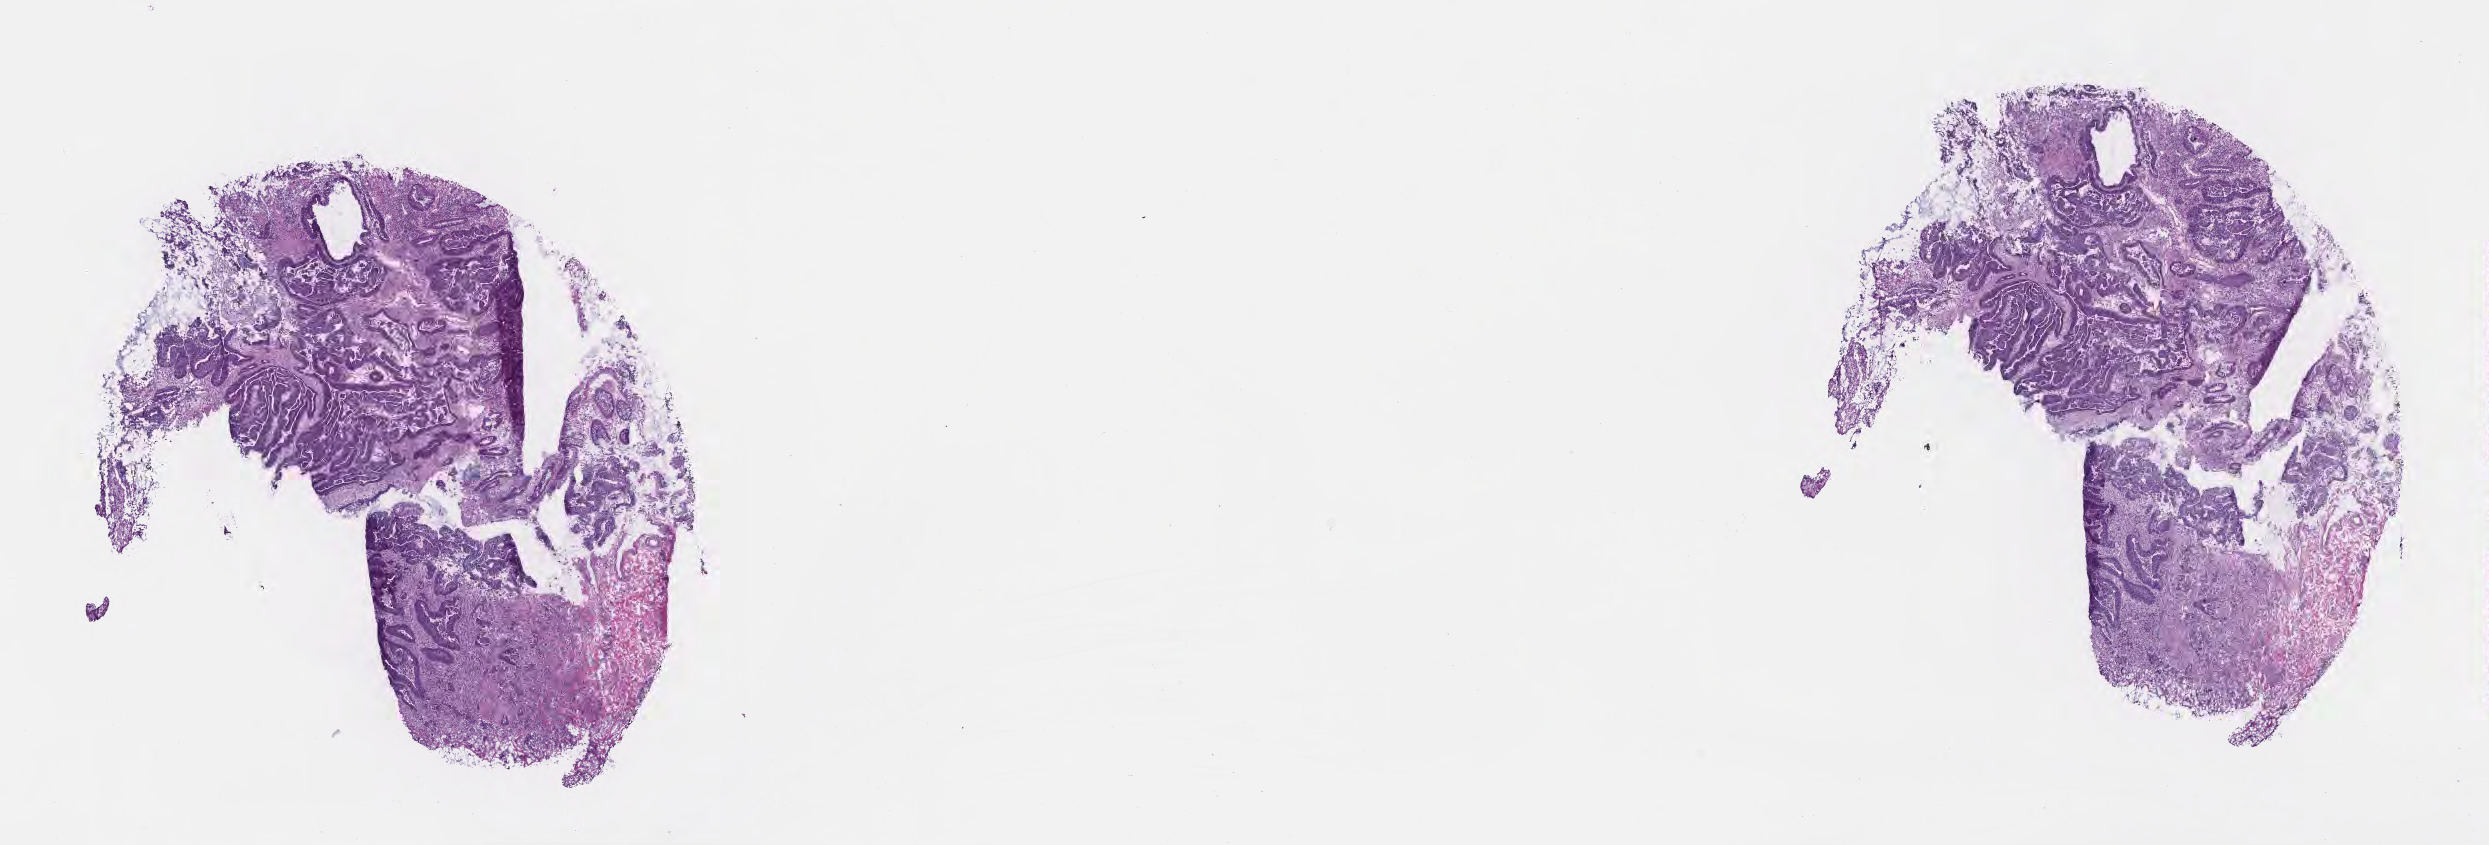
Digitized haematoxylin and eosin-stained section, low-resolution overview of the scanned area, about 20.1 x 6.8 mm. Frozen section. Specimen: primary tumor. Anatomic site: sigmoid colon. Male, age 61 years at initial diagnosis. Tumor grade: GB (borderline). Slide review estimates, as recorded: tumor cells 80%, tumor nuclei 80%, stromal cells 19%, necrosis 1%, normal cells 0%. Inflammatory infiltration, as recorded: lymphocyte infiltration 4%, monocyte infiltration 3%, neutrophil infiltration 7%.
• diagnosis: Adenocarcinoma, NOS
• AJCC pathologic stage: Stage IIIB